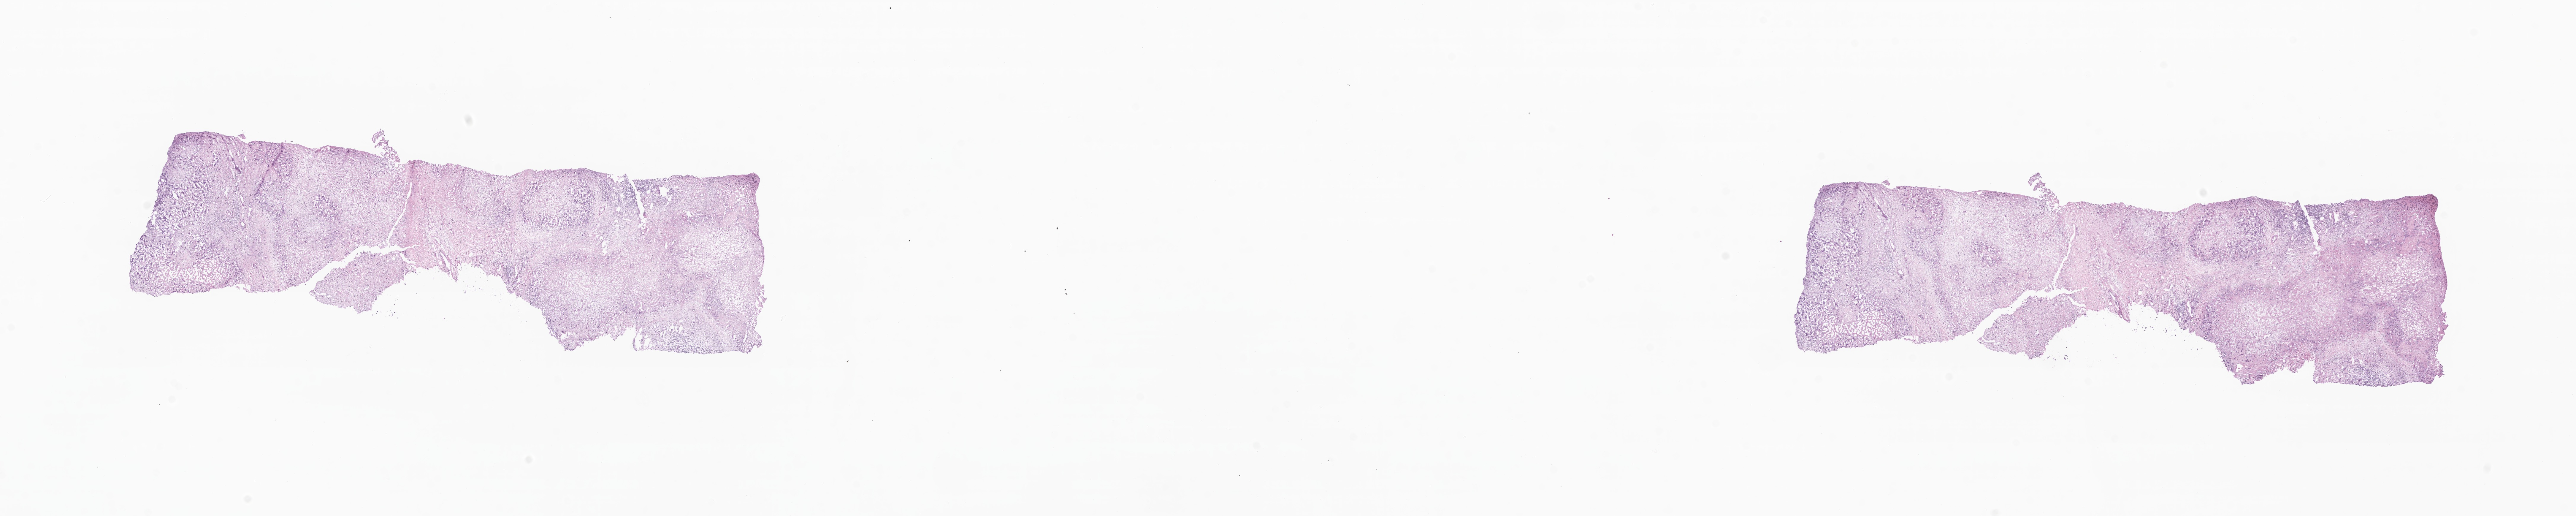
Digitized hematoxylin and eosin (H&E)-stained section, shown as a low-resolution overview of the whole scanned area (about 36.6 x 7.3 mm); frozen section; primary tumor; site: liver. Male patient; age at initial diagnosis 77 years. Slide review estimates, as recorded: tumor cells 23%, tumor nuclei 46%, stromal cells 50%, necrosis 0%, normal cells 27%. Infiltration values recorded for this section: lymphocyte infiltration 12%, monocyte infiltration 0%, neutrophil infiltration 0%.
AJCC pathologic stage: Stage II. Histologic diagnosis: Cholangiocarcinoma.